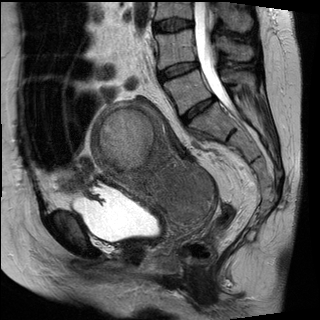
Pelvic MRI for cervical cancer, one sagittal slice. Slice 15 of 30 in the series (ordered by position). T2-weighted. 1.5 T. TE 89 ms, TR 2930 ms. 4 mm slice thickness. 320 × 320 image matrix, field of view 260 × 260 mm. Female patient, age 62 years.
Structures marked on this image (manually delineated by an expert):
- uterus and cervix: bounding box <91,99,212,224> (left, top, right, bottom; pixels)